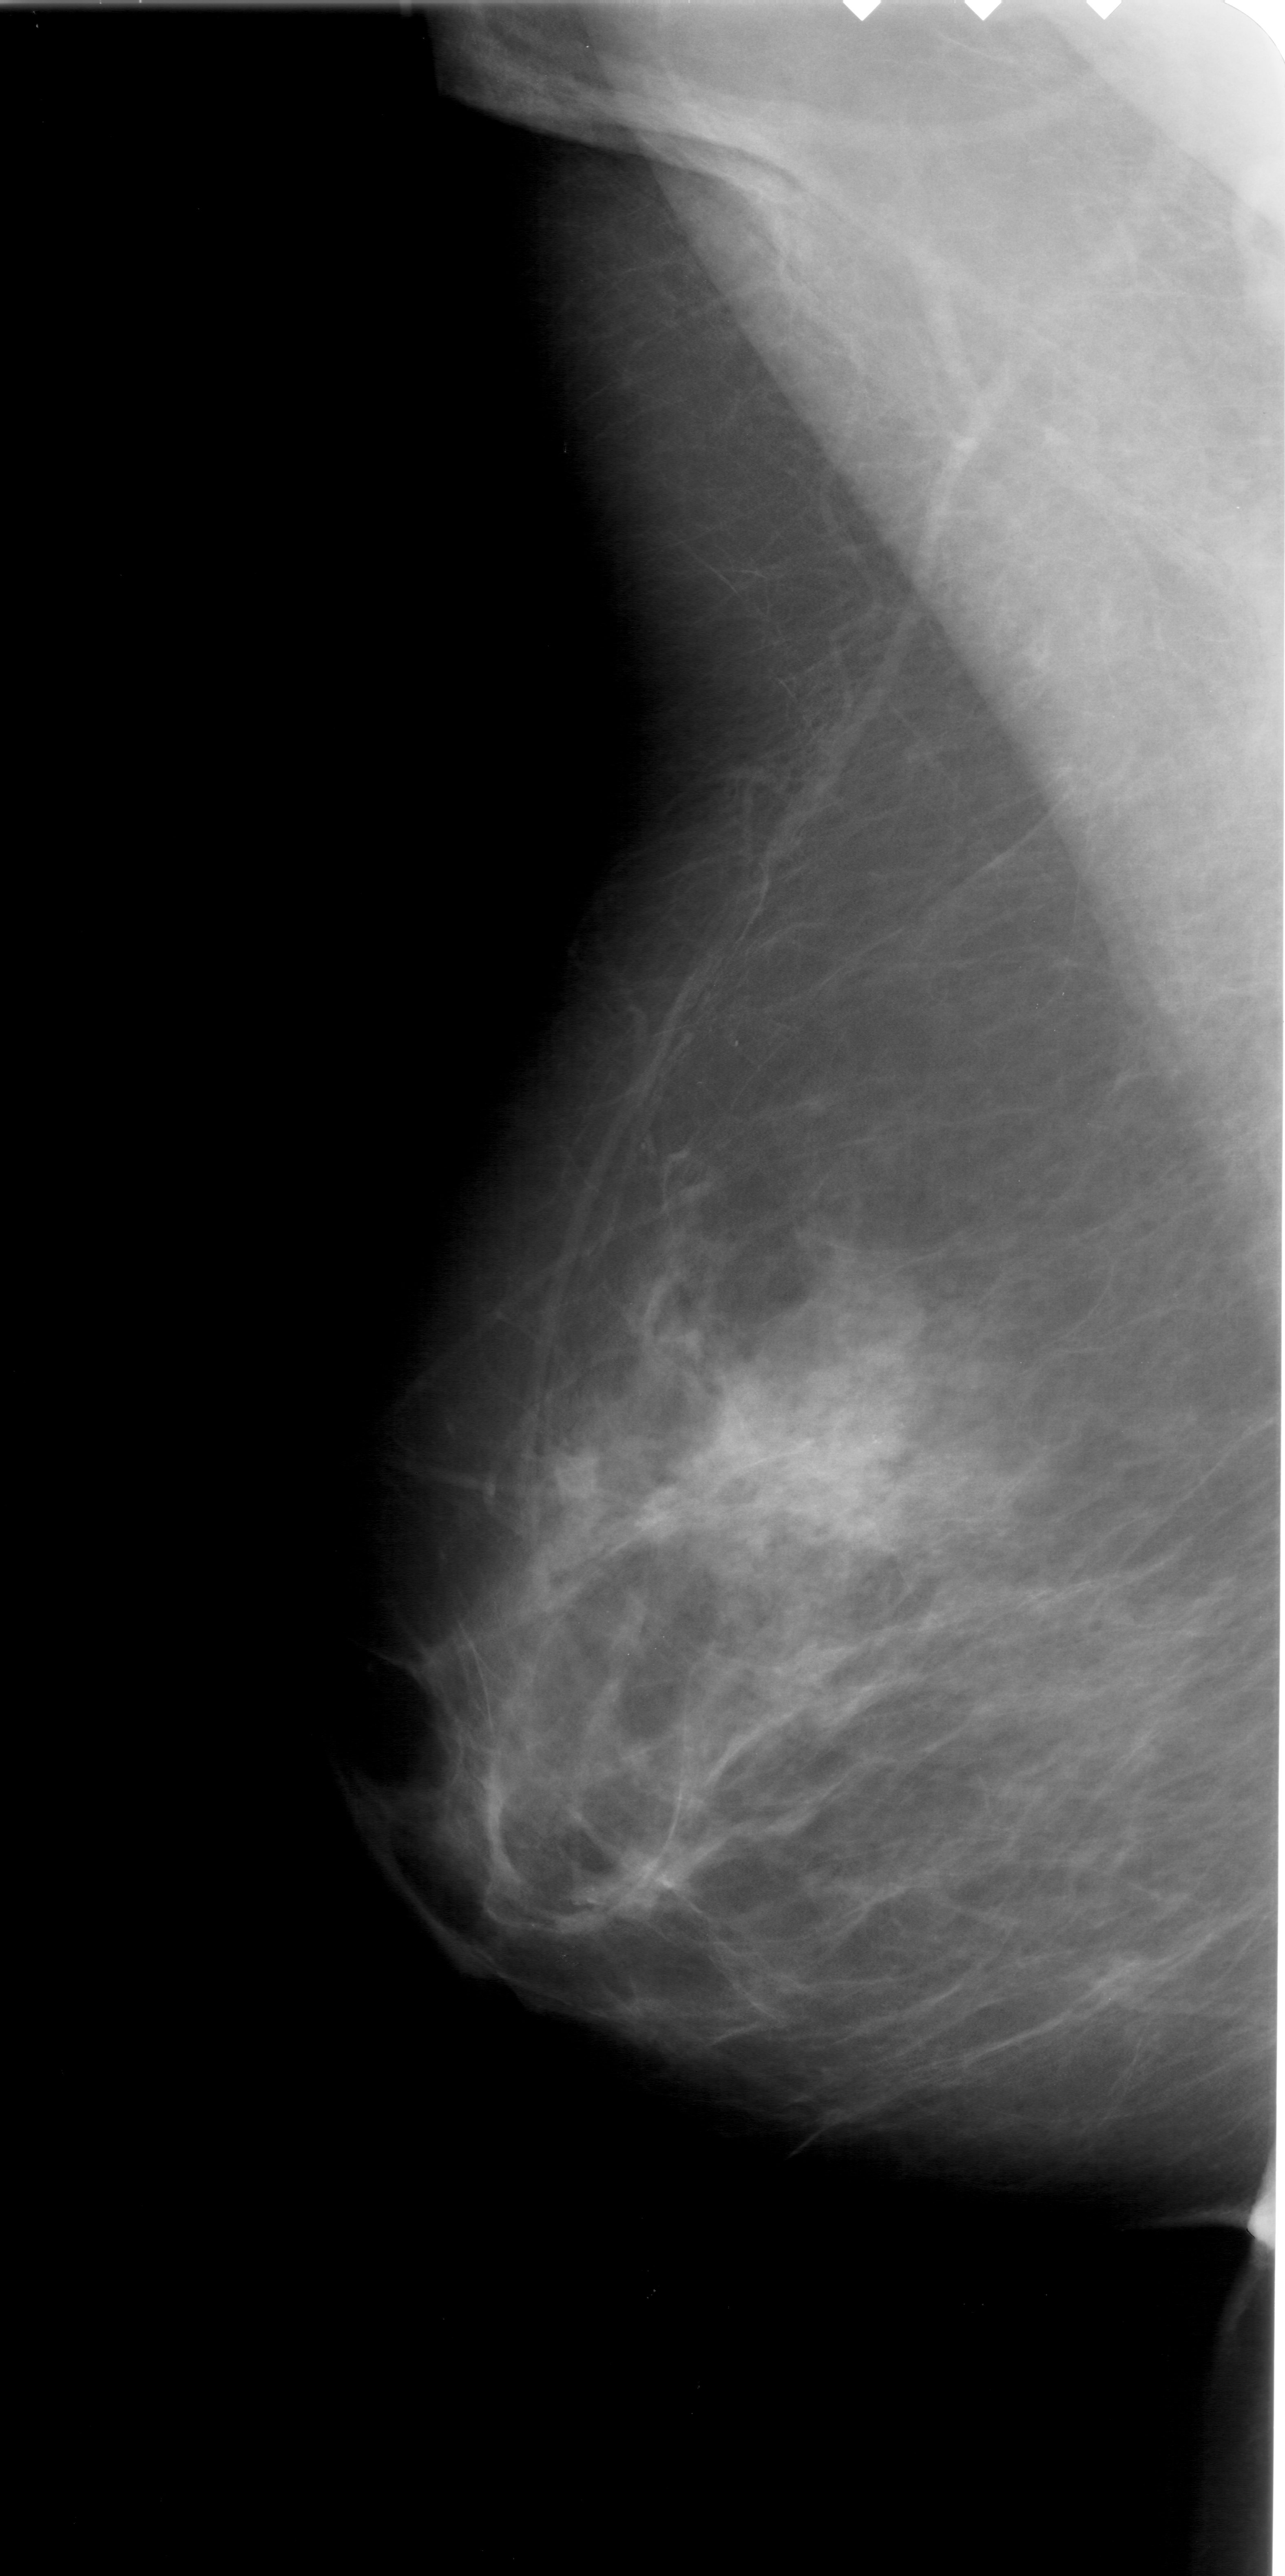
Digitized screen-film mammogram. Left breast. Mediolateral oblique (MLO) view. Breast composition: heterogeneously dense (BI-RADS density category 3 of 4). 1285 × 2576 image matrix.
Marked abnormalities (boxes around the expert regions of interest):
- calcifications, morphology pleomorphic, distribution clustered; BI-RADS assessment category 4; subtlety rating 3 on a 1 (subtle) to 5 (obvious) scale; pathology (as recorded): malignant: bounding box (x1, y1, x2, y2) in pixels: (782, 1349, 989, 1503)